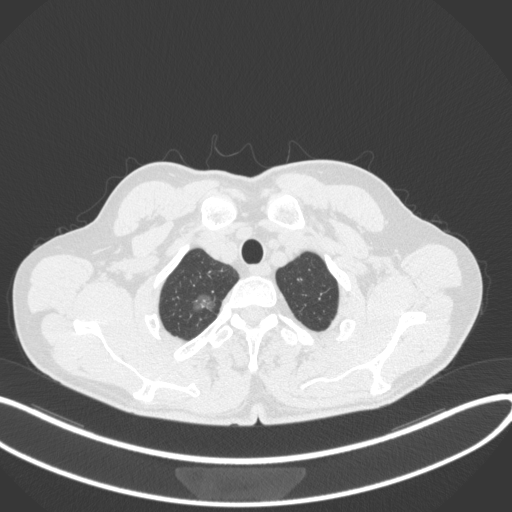
Chest CT, one axial slice; slice 348 of 407 in the series (ordered by position); reconstruction kernel B31f; 120 kVp; lung window (W 1500 / L -600 HU); 512 × 512 image matrix, field of view 400 × 400 mm. Patient: male, 58 years. From the clinical record (not read from this slice): clinical TNM (as recorded): T1c N0 M0; histopathological grade: G1-2.
Annotated regions visible in this slice (rectangle marked by the reading radiologist):
- lung tumour (recorded histology: adenocarcinoma): bounding box (x1, y1, x2, y2) in pixels: (190, 293, 222, 321)